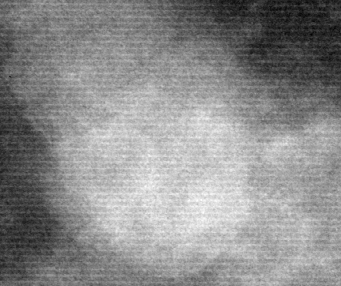
Cropped region of a digitized screen-film mammogram centred on a radiologist-marked abnormality; left breast; CC view; BI-RADS breast density category 2 (scale 1–4).
Marked abnormality: mass, shape lobulated, margins circumscribed; BI-RADS assessment category 3; subtlety rating 4 on a 1 (subtle) to 5 (obvious) scale; pathology (as recorded): benign.